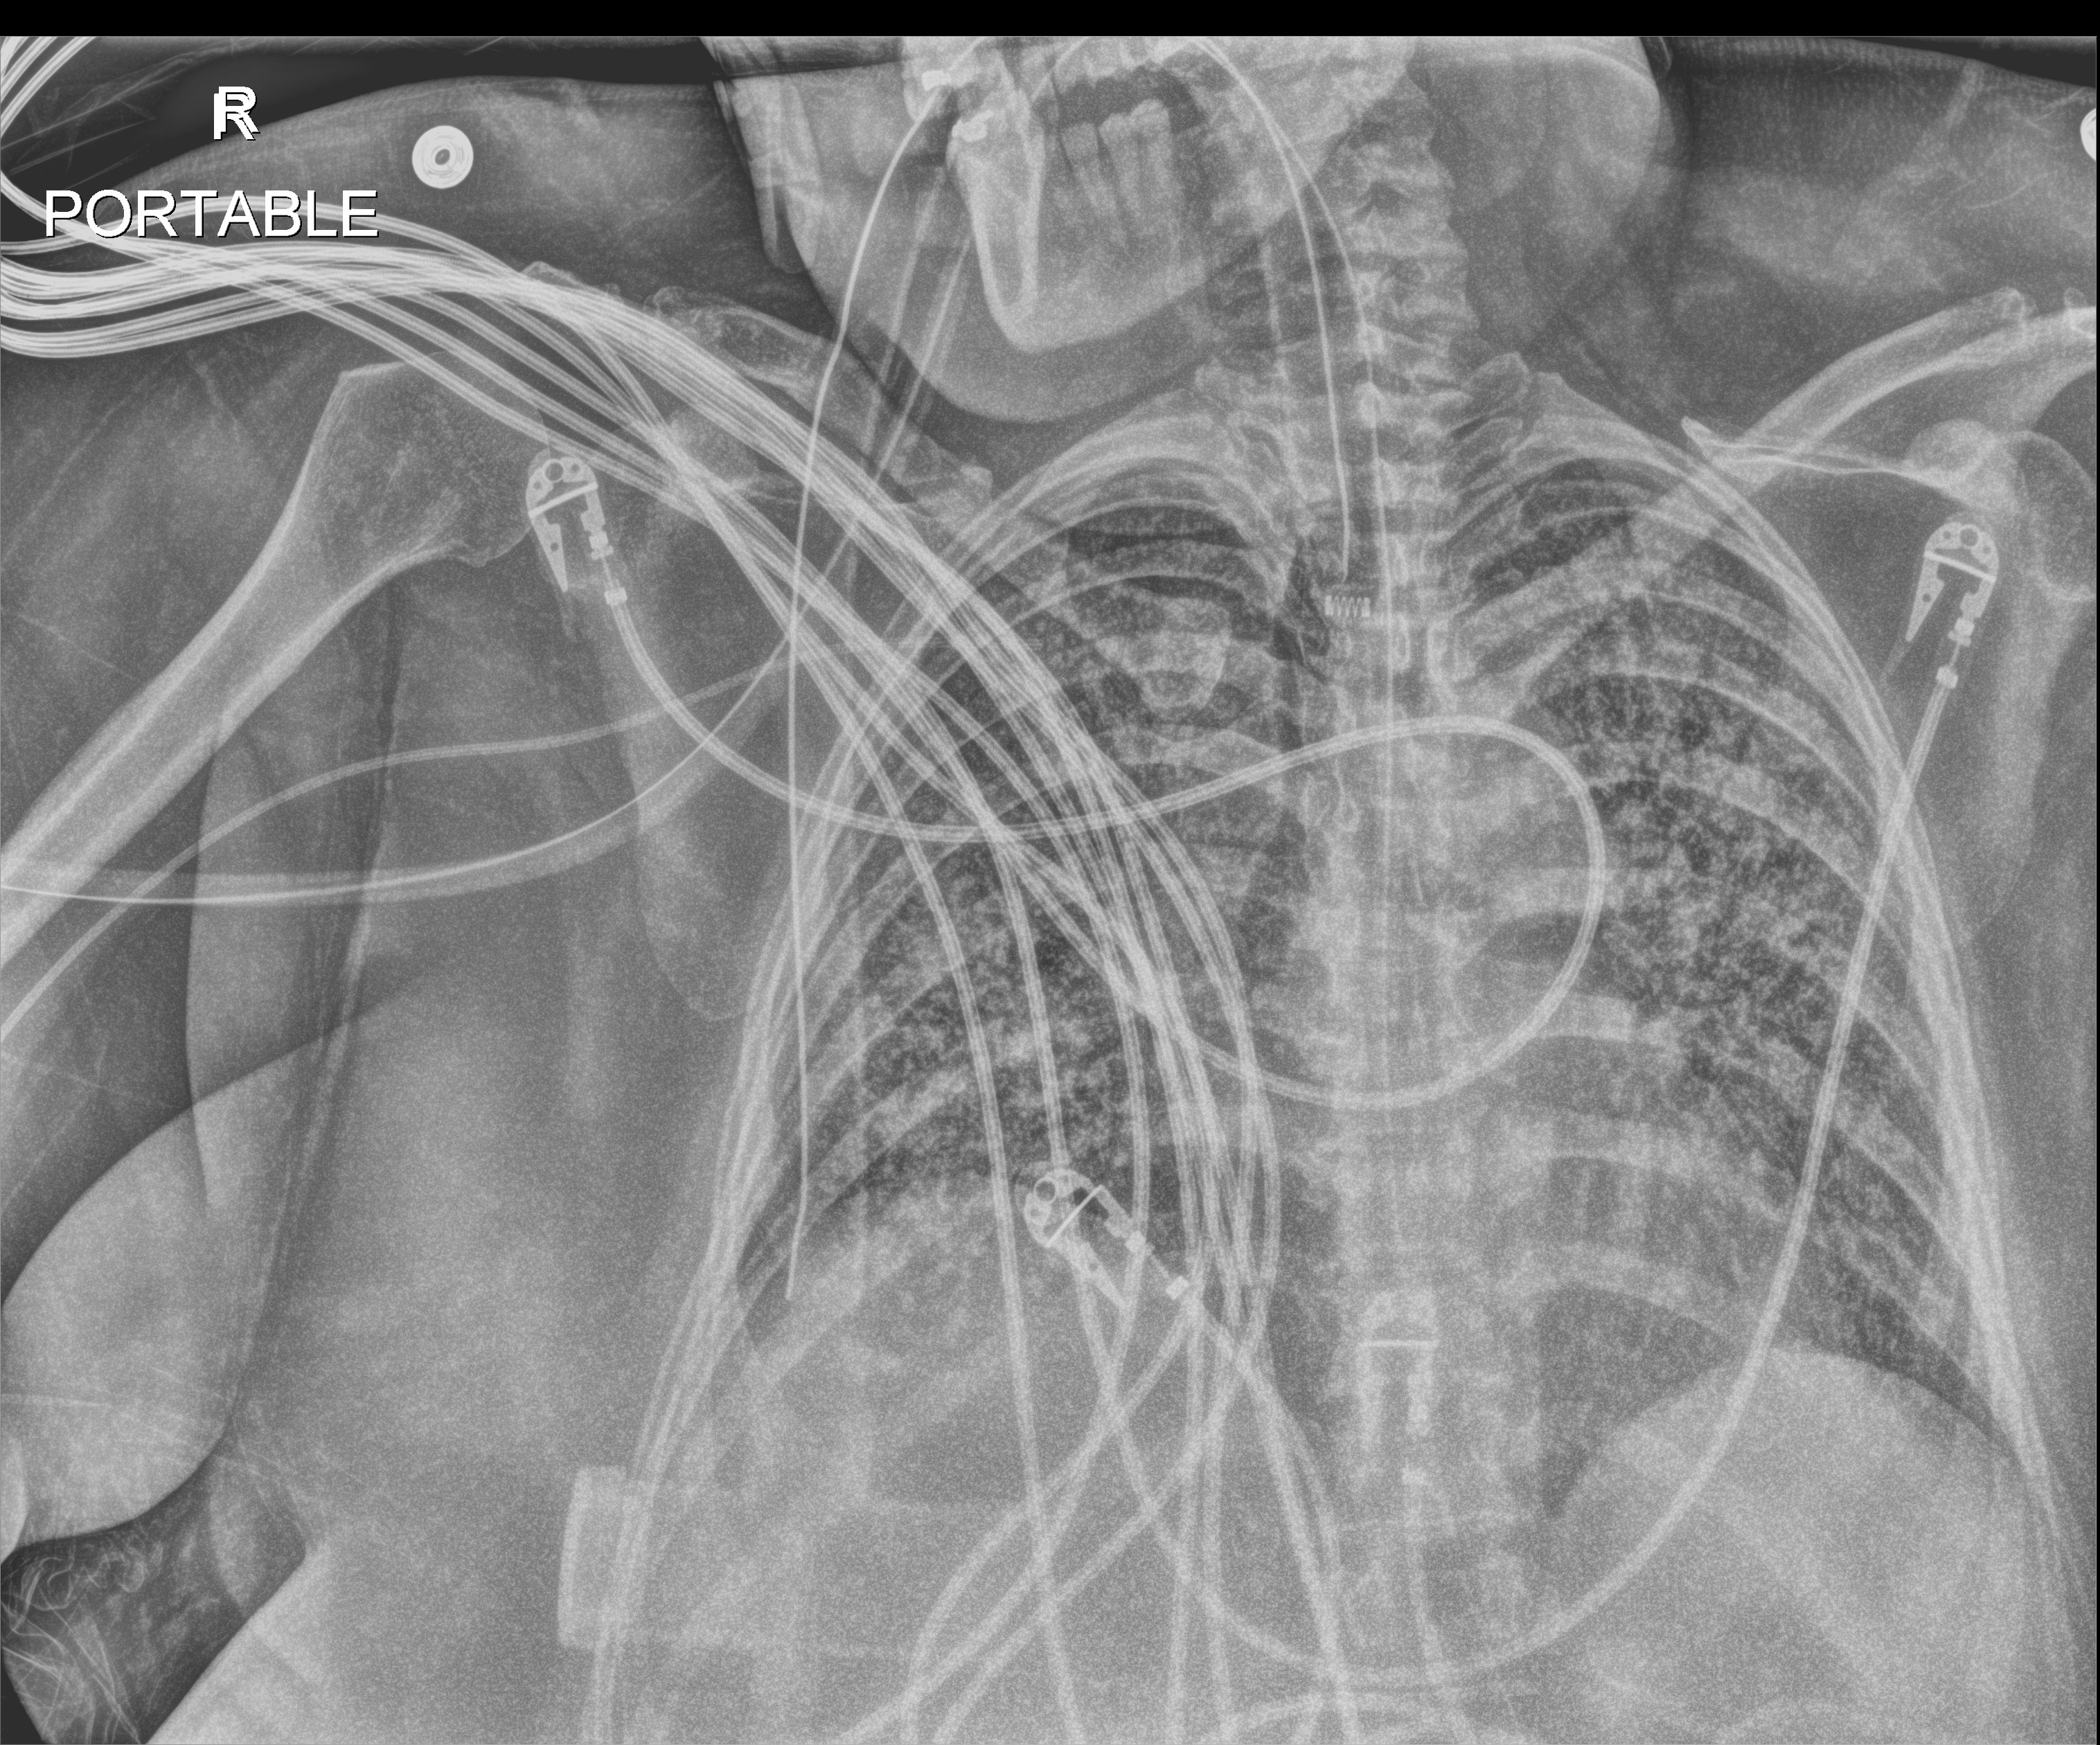
Chest X-ray (portable); anteroposterior (AP) projection. Patient hospitalised with COVID-19; female, aged 18–59 years.
Hospital-stay facts (about this admission, not read from this image; timing relative to this image not recorded): admitted to intensive care during this hospital stay: yes.